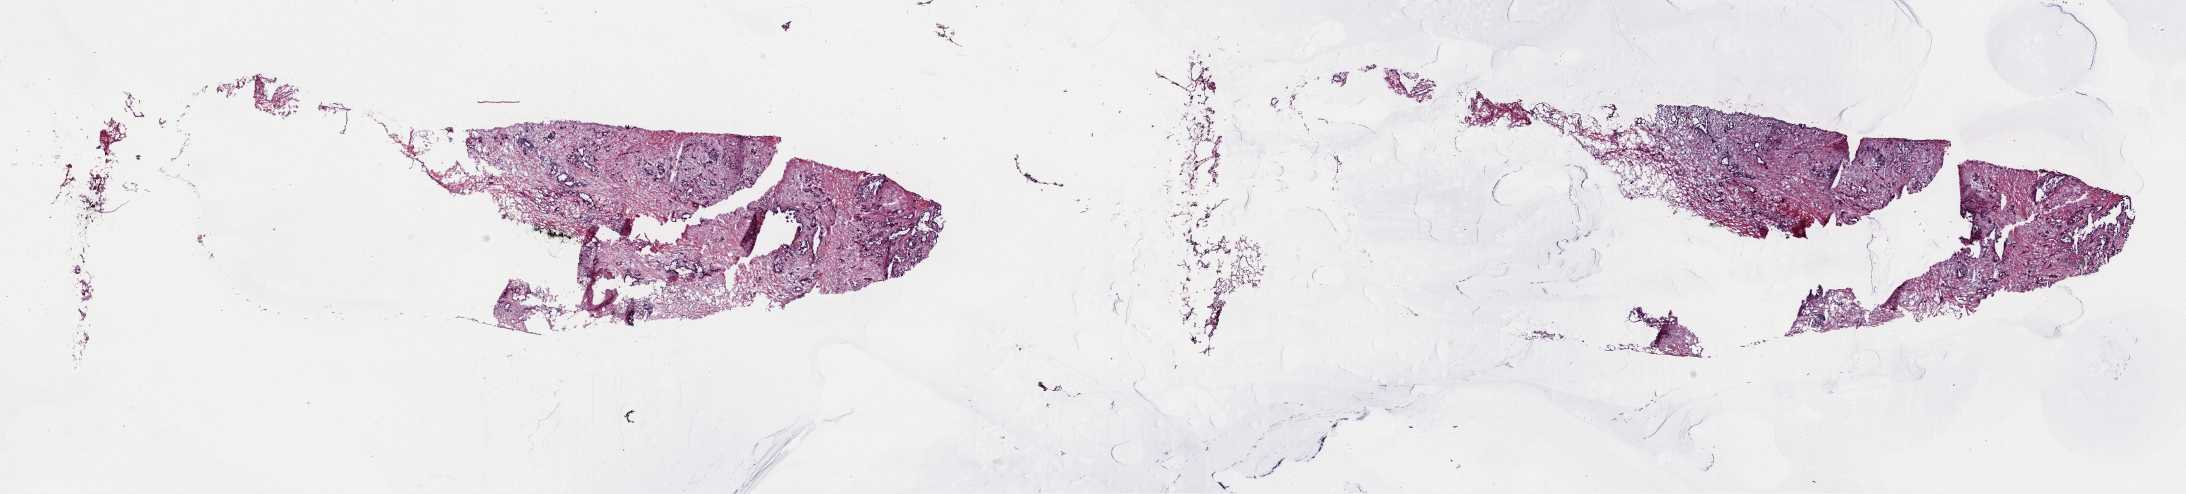
Digitized H&E tissue section (whole slide), low-resolution overview of the scanned area, about 34.5 x 7.8 mm (acquisition: 40x scan); frozen section from the top of the tissue portion; sample: primary tumour, pancreas. Male, age 75 years at initial diagnosis. Histologic grade: G3 (poorly differentiated). Pathologist review of this section (percent, as recorded): tumour cells 30%, tumour nuclei 50%, normal cells 0%, stromal cells 65%, necrosis 5%. Infiltration values recorded for this section: lymphocyte infiltration 3%, monocyte infiltration 0%, neutrophil infiltration 0%.
AJCC pathologic stage: IIB (7th edition). Histologic diagnosis: Infiltrating duct carcinoma, NOS (head of pancreas). Lymph nodes positive (case pathology): 4 of 10 examined.